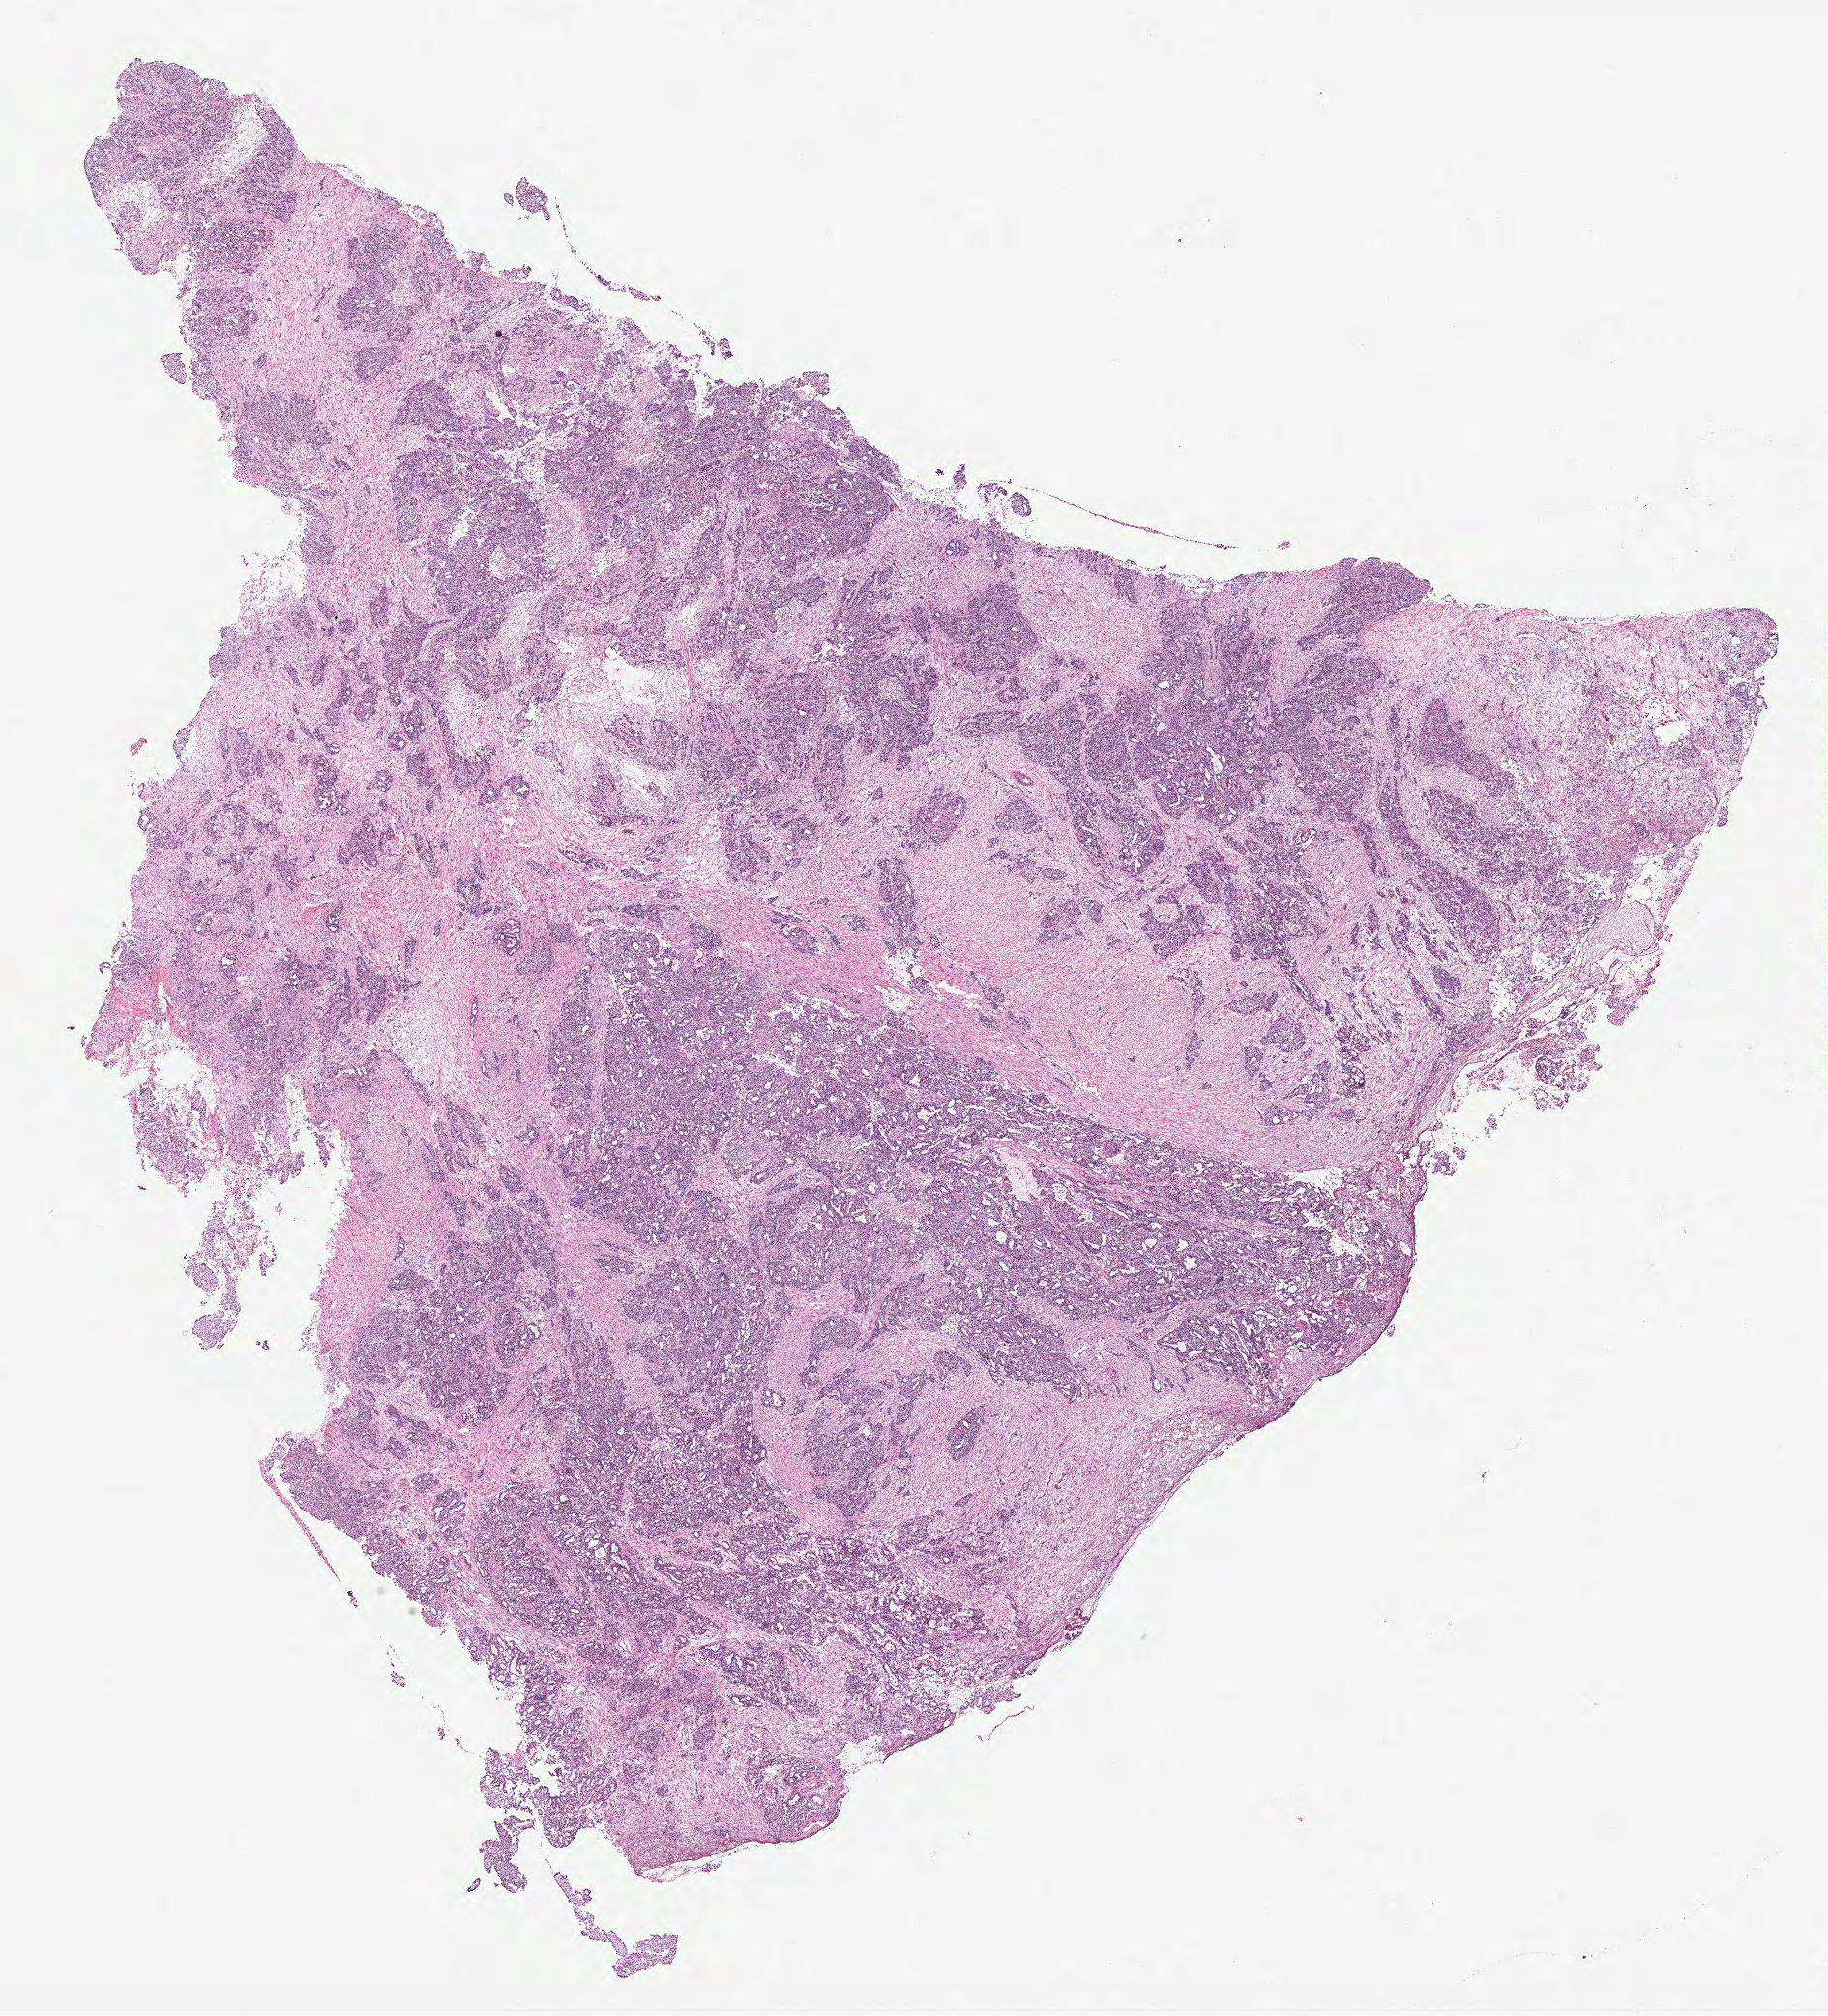
Whole-slide histology image, Hematoxylin and eosin (H&E) stained, shown as a low-resolution overview of the whole scanned area (about 15.1 x 16.7 mm). Ovary, tumour tissue. Female, 37 y/o.
* histologic diagnosis: Serous adenocarcinoma, NOS
* primary tumour site (as recorded): ovary